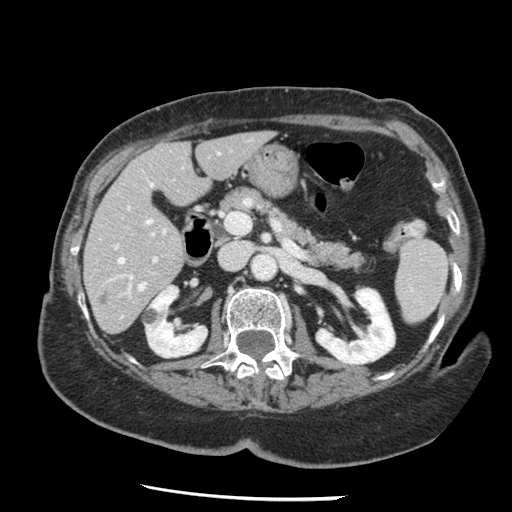
Contrast-enhanced abdominal CT, one axial slice. Reconstruction kernel STANDARD. Intravenous contrast given. Soft-tissue window (W 400 / L 40 HU). 2.5 mm slice thickness. 512 × 512 image matrix. Female patient, age 85 years. Case-level facts recorded for this patient, not image findings: diagnosis: colorectal cancer liver metastases, imaged before liver resection; multiple liver metastases: no; largest metastasis: 0.9 cm; chemotherapy before resection: yes.
Structures marked on this image (manually delineated by an expert):
- hepatic veins: bounding box [x1, y1, x2, y2] px = [118, 221, 150, 290]
- liver: [84, 133, 271, 333]
- planned liver remnant (the part of the liver to remain after resection): [84, 133, 271, 323]
- portal vein (with intrahepatic branches): [116, 207, 158, 285]
- liver metastasis: [99, 293, 111, 304]